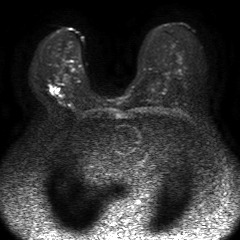
Breast MRI, one axial slice. Position 31 of 50 along the scan axis. Diffusion-weighted series; image 2 of 4 stored at this slice position (different b-values; order by instance number). 1.5 T. 4 mm slice thickness. 240 × 240 image matrix, field of view 330 × 330 mm. Female patient.
Annotated regions visible in this slice (expert manual segmentation):
- tumour on diffusion-weighted imaging: box from (x=49, y=88) to (x=56, y=94) px